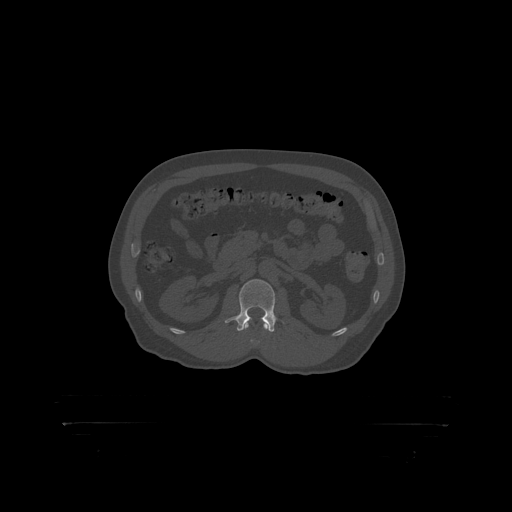
CT including the spine, one axial slice. Position 304 of 399 along the scan axis. 120 kVp. Bone window (W 1800 / L 400 HU). 1.25 mm slice thickness. 512 × 512 image matrix, field of view 650 × 650 mm. Male patient, age 46 years. From the clinical record (not read from this slice): primary cancer: skin.
Structures marked on this image (semi-automatic segmentation, software-assisted and operator-edited):
- L2 vertebra: bounding box <239,280,276,319> (left, top, right, bottom; pixels)